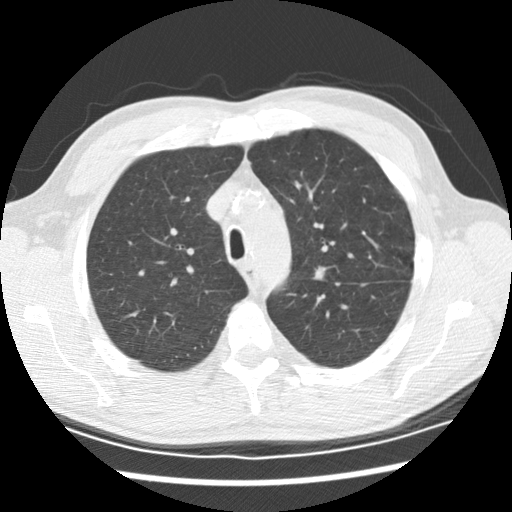
Chest CT (low-dose screening protocol), one axial image, second annual screen, lung window (W 1500 / L -600 HU), 2.5 mm slice thickness, 120 kVp, slice 55 of 208 in the series. Male, age 59 years at enrolment. Current smoker at enrolment.
- Expert-annotated lung lesion, bounding box <302,261,337,292> (left, top, right, bottom; pixels).
- The exam's reader record, not a measurement of the box and not confirmed to be the same lesion: non-calcified nodule or mass ≥4 mm, left upper lobe, 8 × 7 mm, spiculated (stellate) margins, soft tissue attenuation, pre-existing on the prior screen: yes; interval growth: yes.
- Official screen result: positive, change unspecified: nodule(s) >= 4 mm or enlarging nodule(s), mass(es), or other non-specific abnormalities suspicious for lung cancer.
- Lung cancer was diagnosed 251 days after this screen: adenocarcinoma, NOS, left upper lobe, left lower lobe, poorly differentiated (G3), stage IV (AJCC 6th edition).